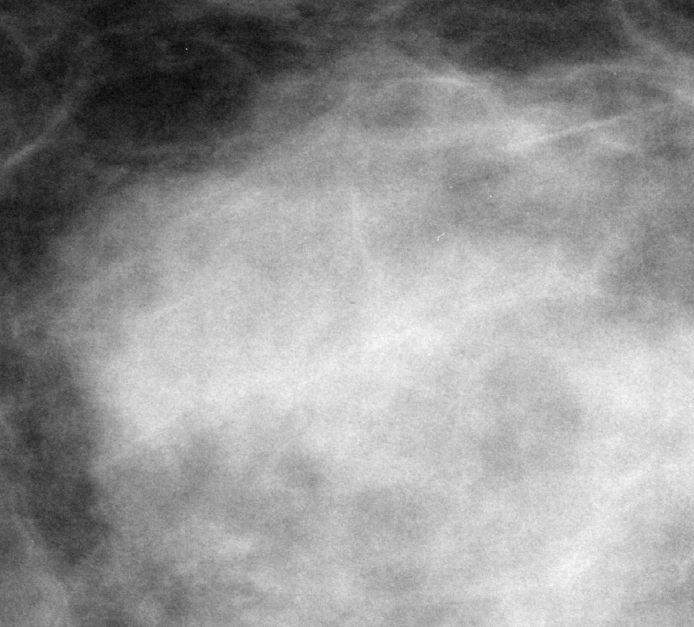
Crop from a digitized film mammogram around one marked abnormality; right breast; CC view.
Finding: mass, shape irregular / focal asymmetric density, margins ill defined; BI-RADS assessment category 3; pathology result (as recorded, not read from the image): benign.